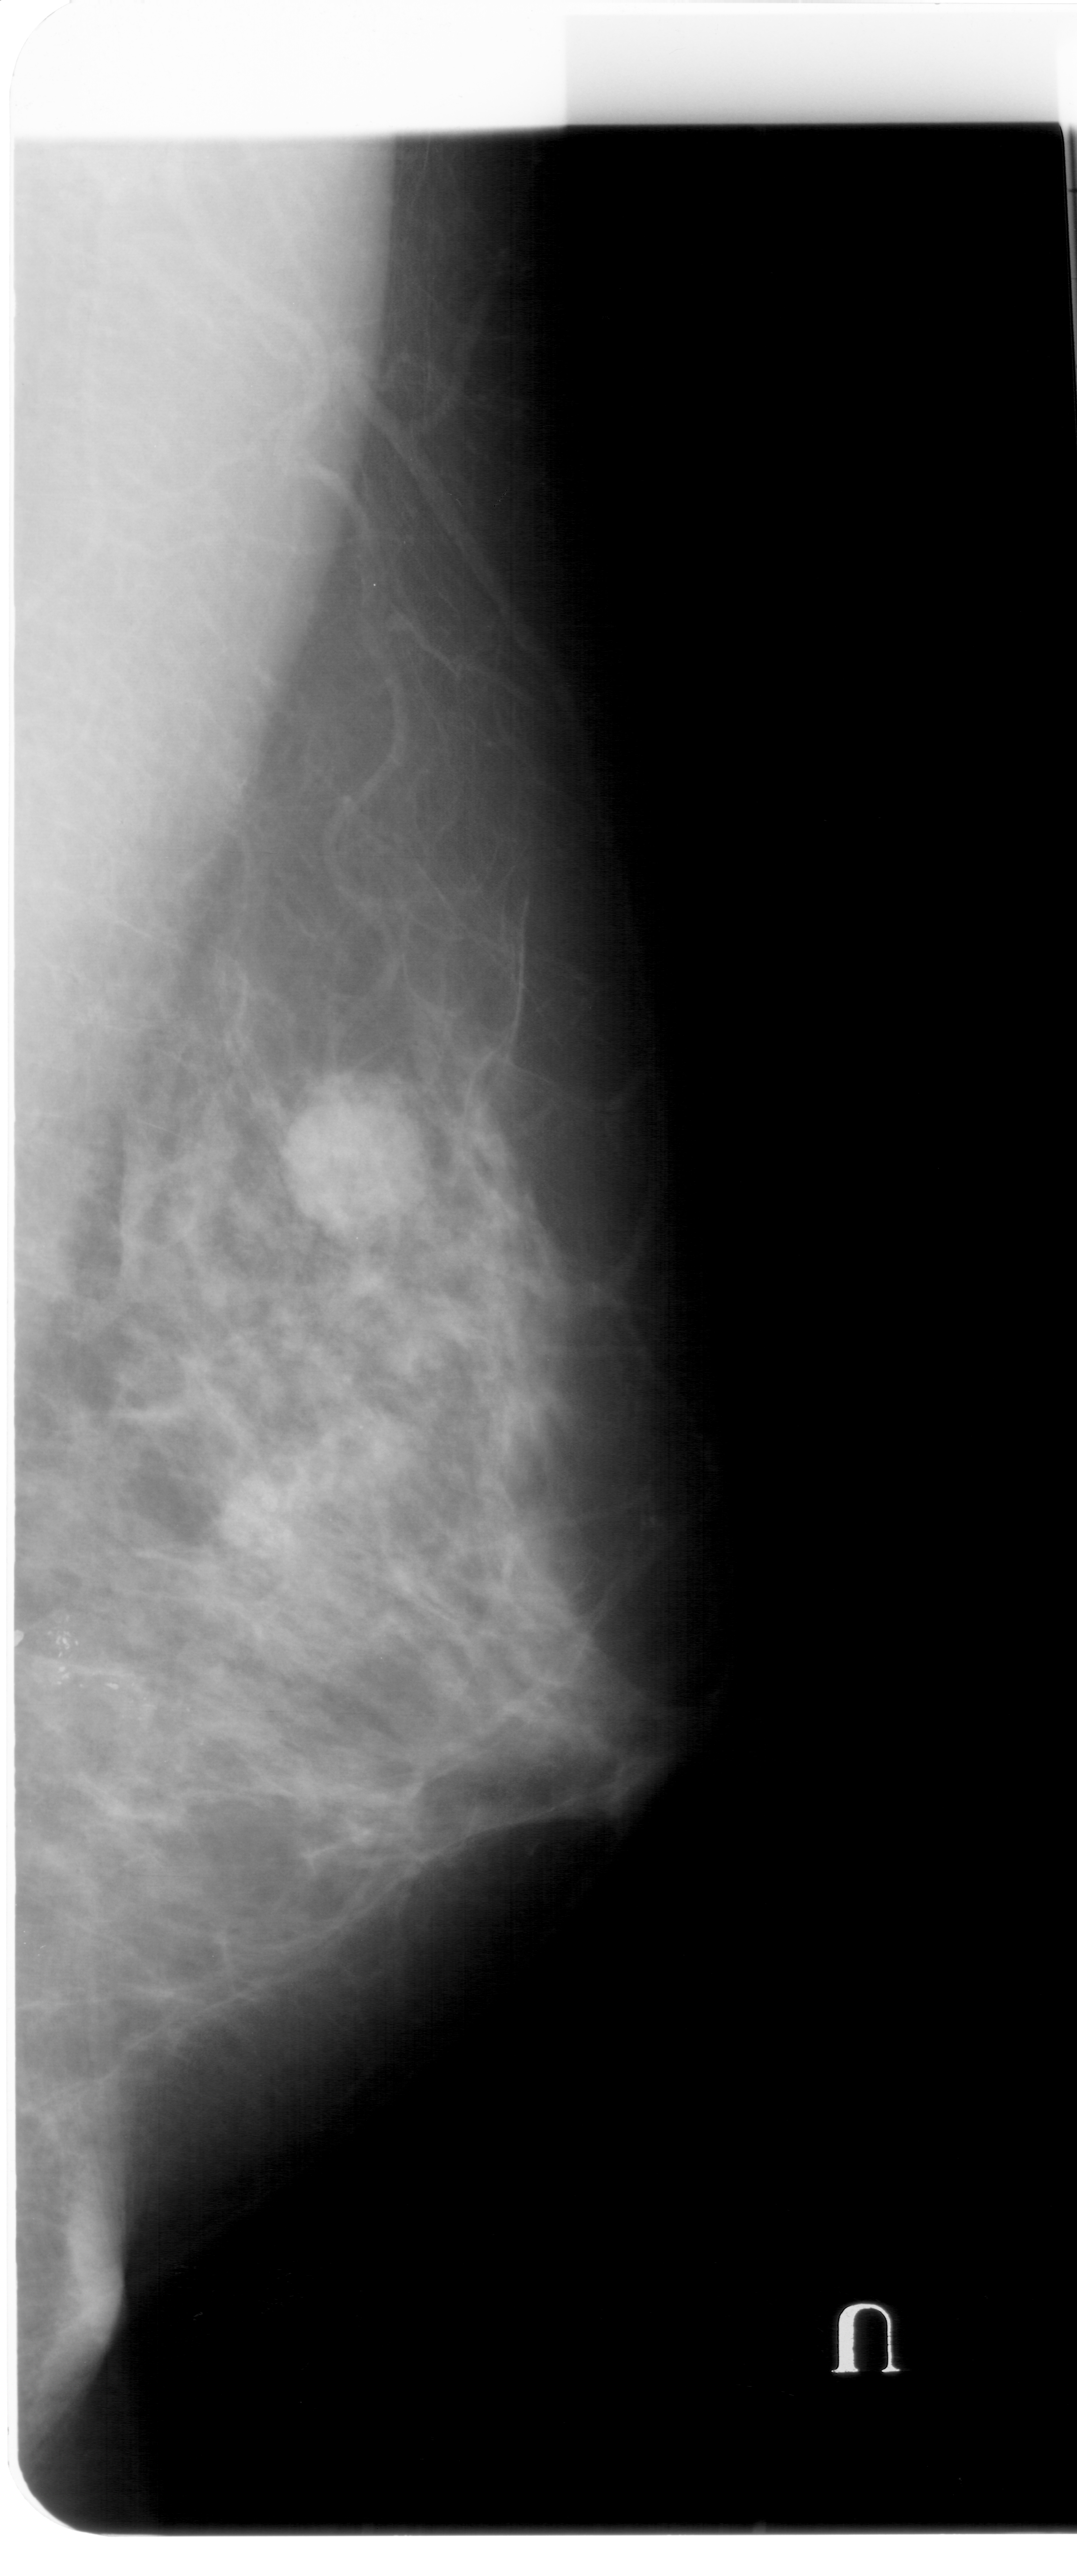
Mammogram (digitized film); right breast; MLO view; breast composition: heterogeneously dense (BI-RADS density category 3 of 4).
Abnormality record for this image: mass, shape round, margins obscured; BI-RADS assessment category 4; pathology result (as recorded, not read from the image): benign.